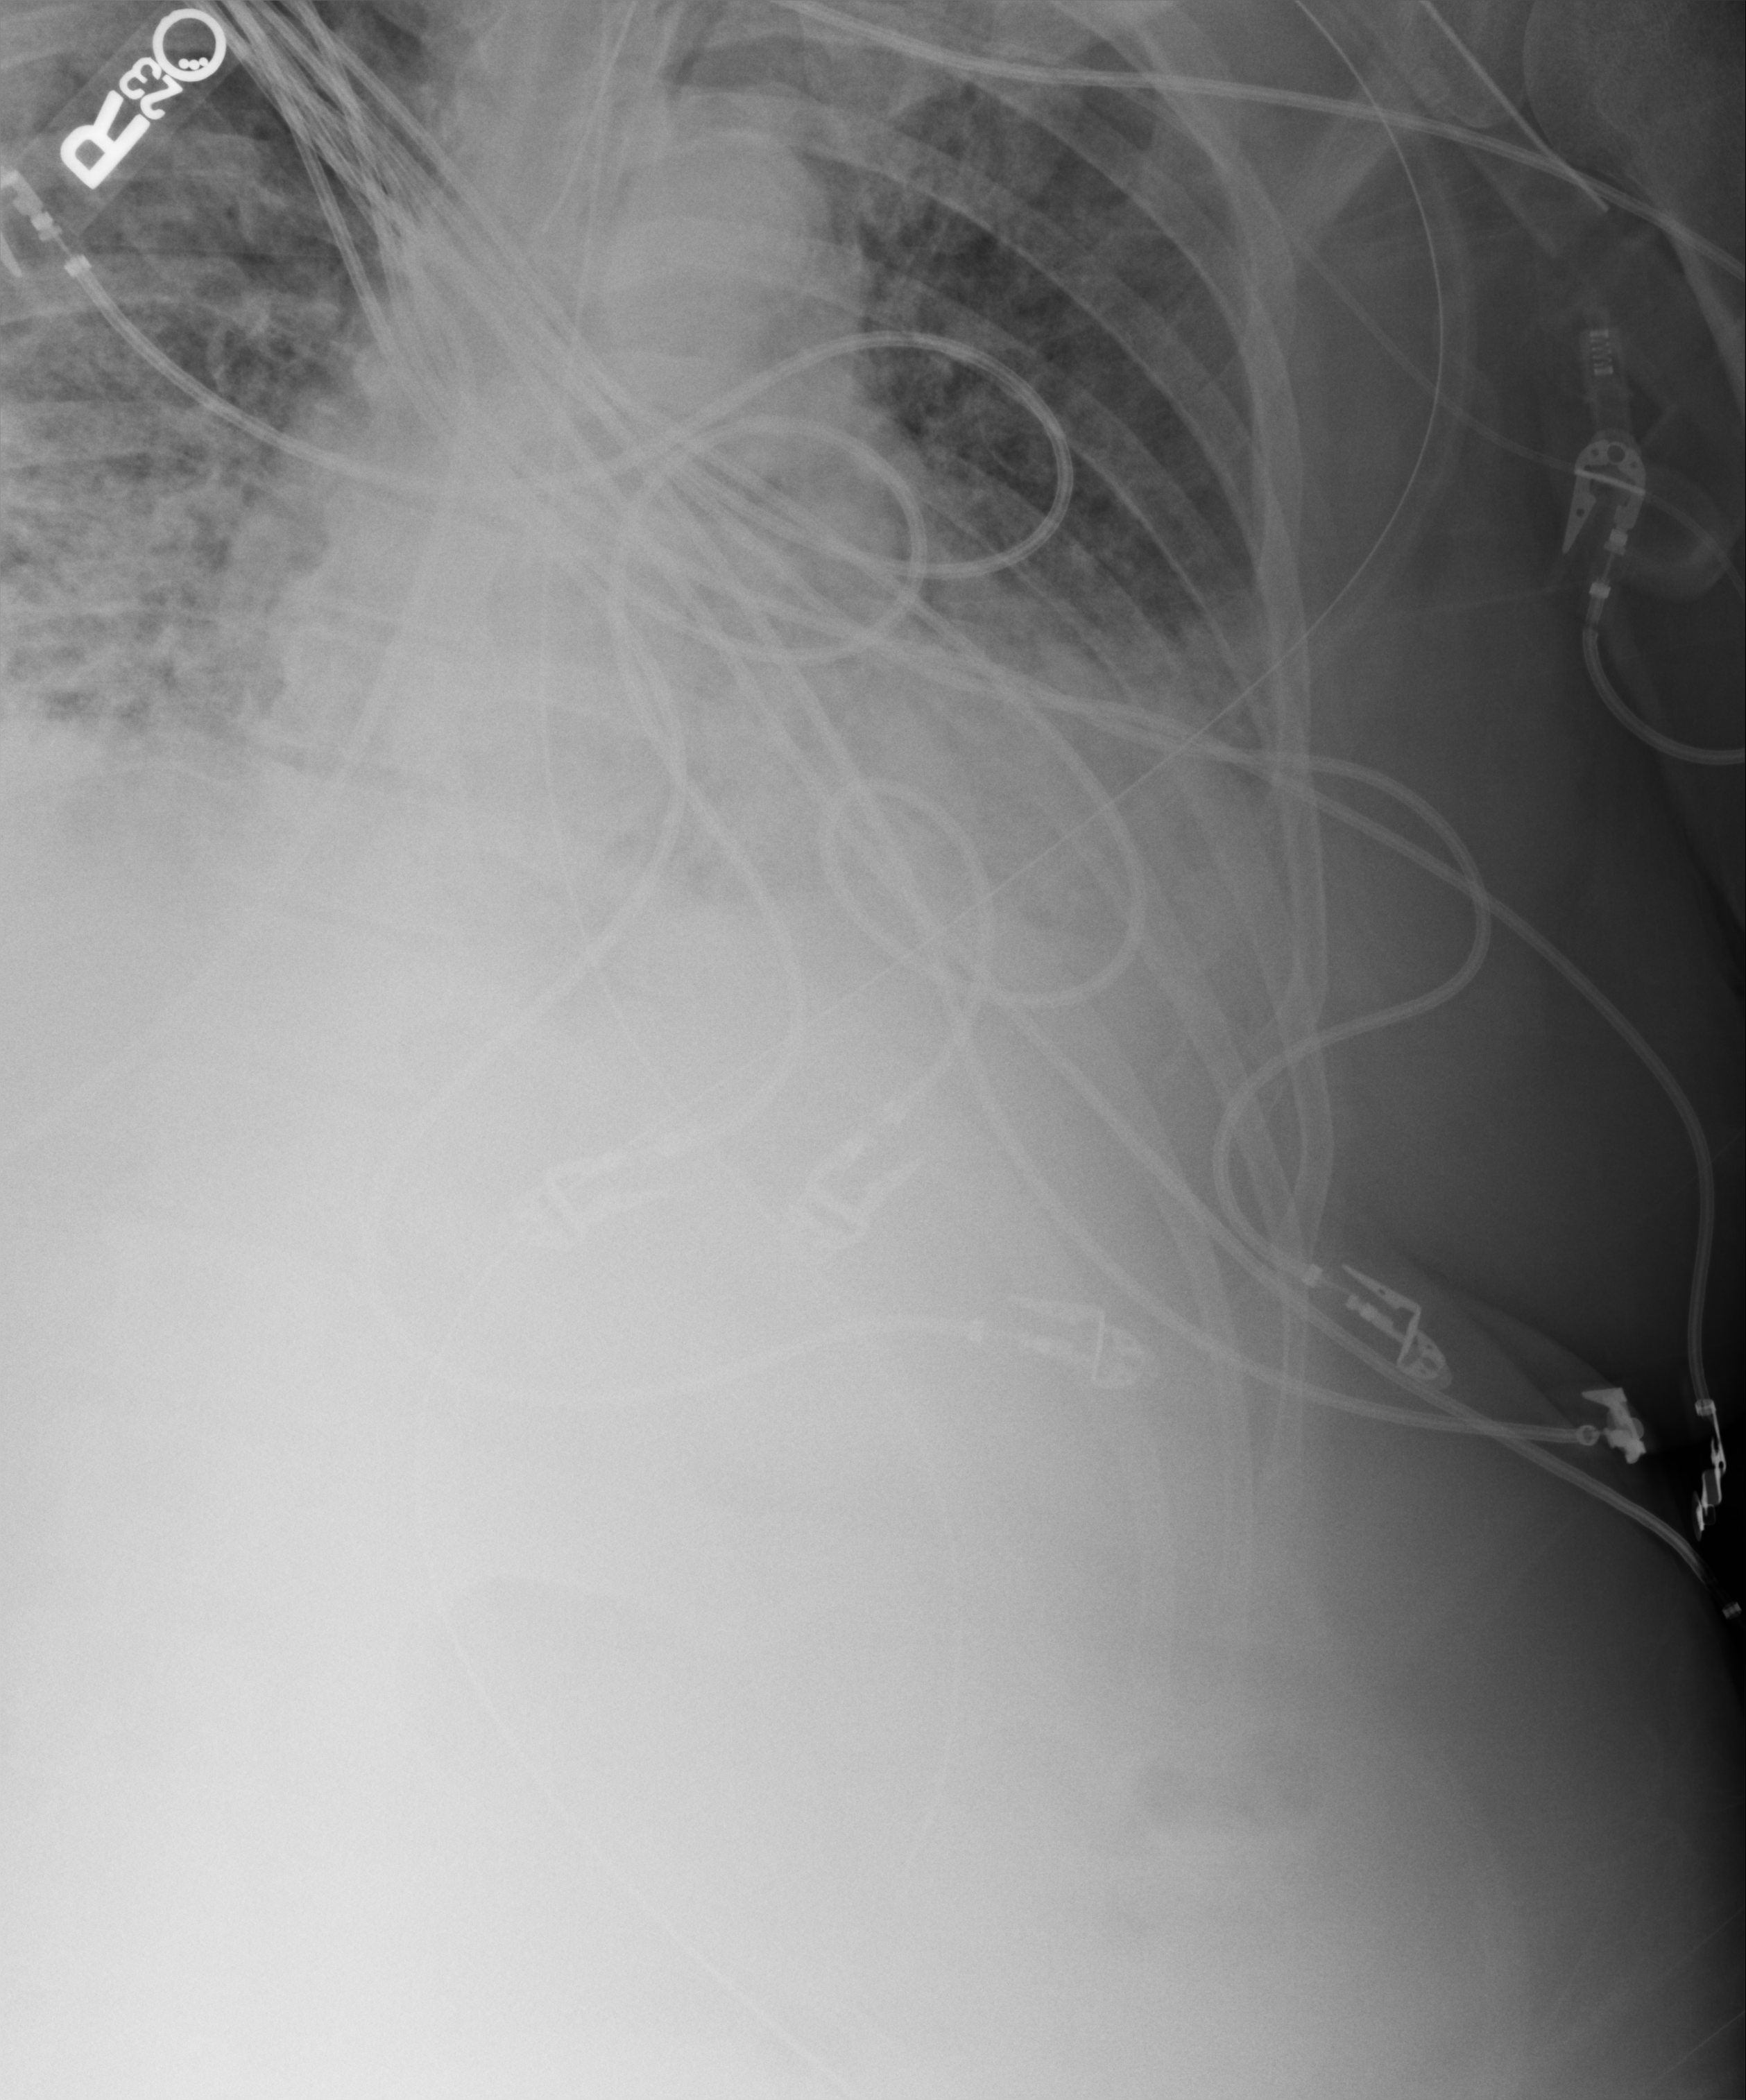
Portable chest radiograph; anteroposterior (AP) projection. Male patient hospitalised with COVID-19, age 60–74 years.
Admission-level facts for this patient (not findings on this image; timing relative to this image not recorded): mechanically ventilated during this hospital stay: yes; smoking status (admission record): former.